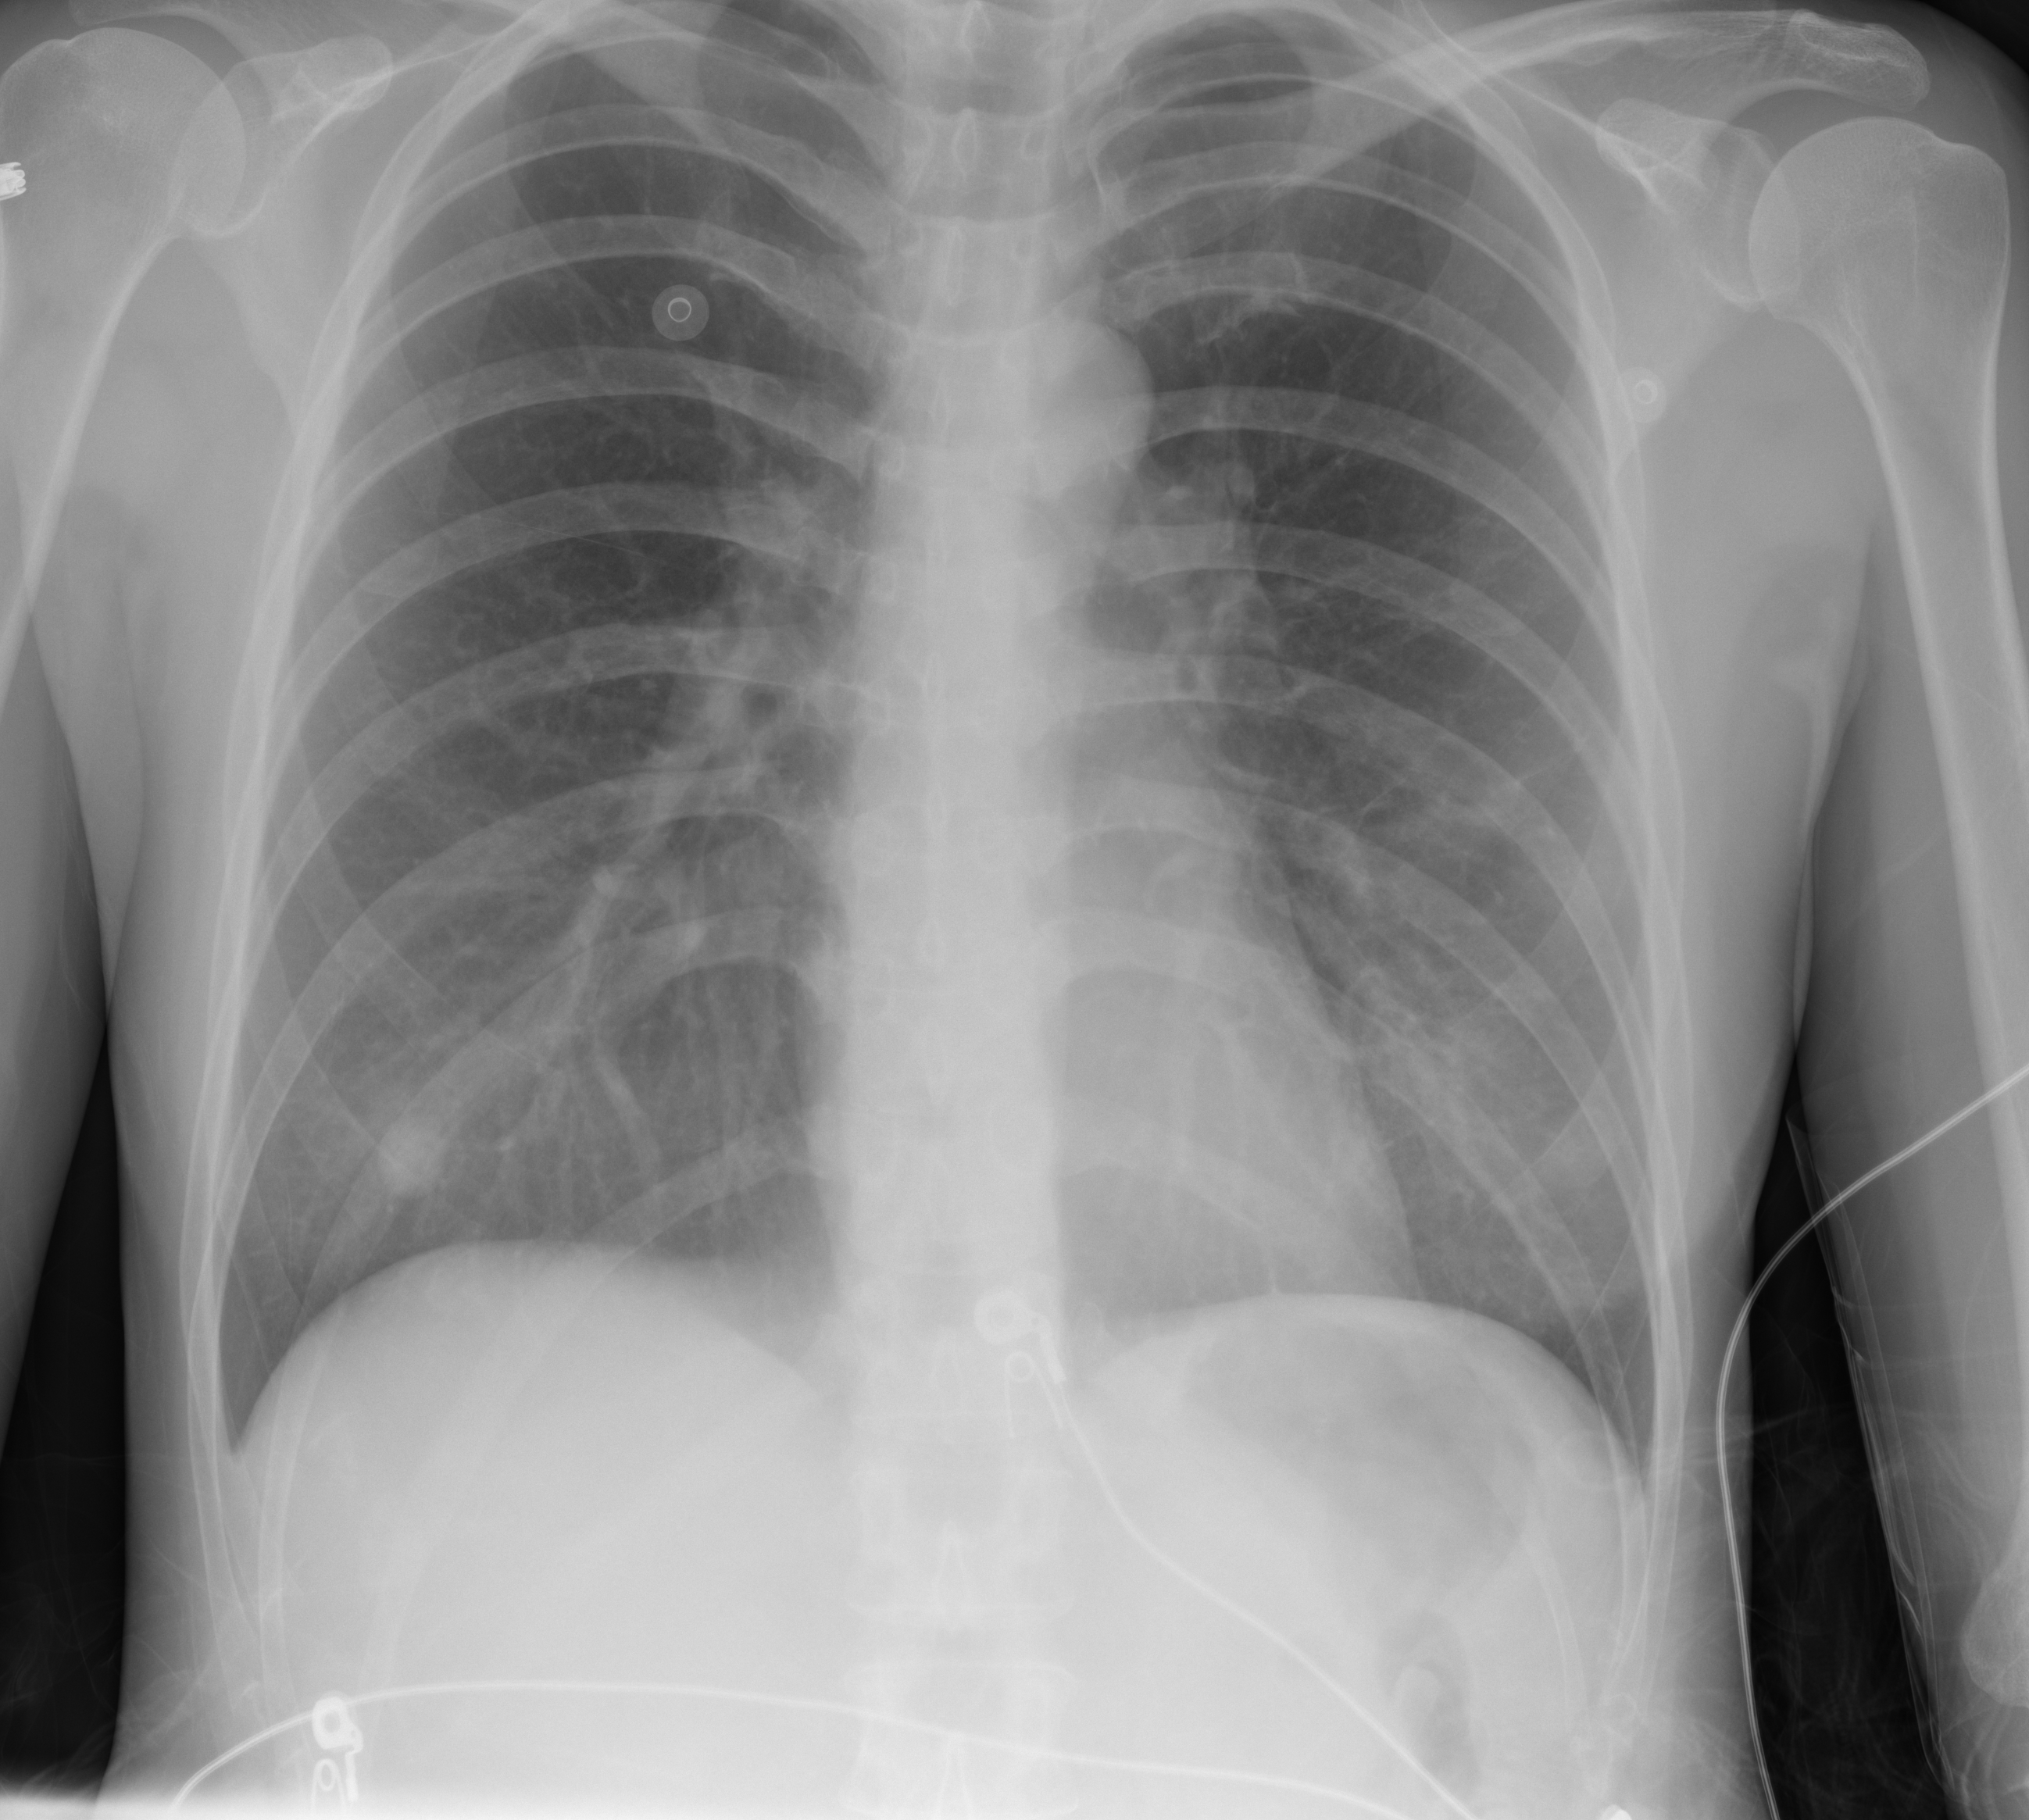
Chest X-ray (portable), AP projection. Female patient, age 41 years; imaged 4 days after the COVID-19 diagnosis.
Radiologist key findings (as recorded): The lungs are clear and well inflated.